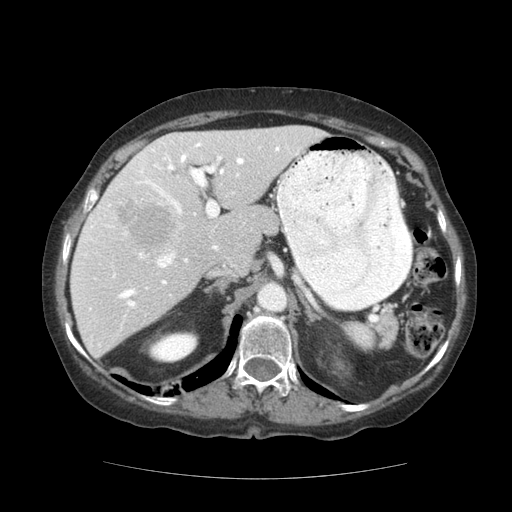
Contrast-enhanced abdominal CT (liver protocol), one axial slice; slice 77 of 111 in the series (ordered by position); reconstruction kernel STANDARD; soft-tissue window (W 400 / L 40 HU); 512 × 512 image matrix, field of view 360 × 360 mm. From the clinical record (not read from this slice): diagnosis: hepatocellular carcinoma (patient treated with transarterial chemoembolisation; whether this scan precedes or follows treatment is not stated here); TNM stage (as recorded): Stage-I; Child-Pugh class: A; tumour nodularity: uninodular; tumour size: 7.3 cm.
Structures marked on this image (semi-automatically segmented with operator editing):
- liver parenchyma outside the tumour (the mass and vessels are separate outlines, so this box may not span the whole liver): bounding box [x1, y1, x2, y2] px = [70, 126, 326, 358]
- mass: [117, 199, 173, 251]
- liver vessels: [84, 141, 298, 310]